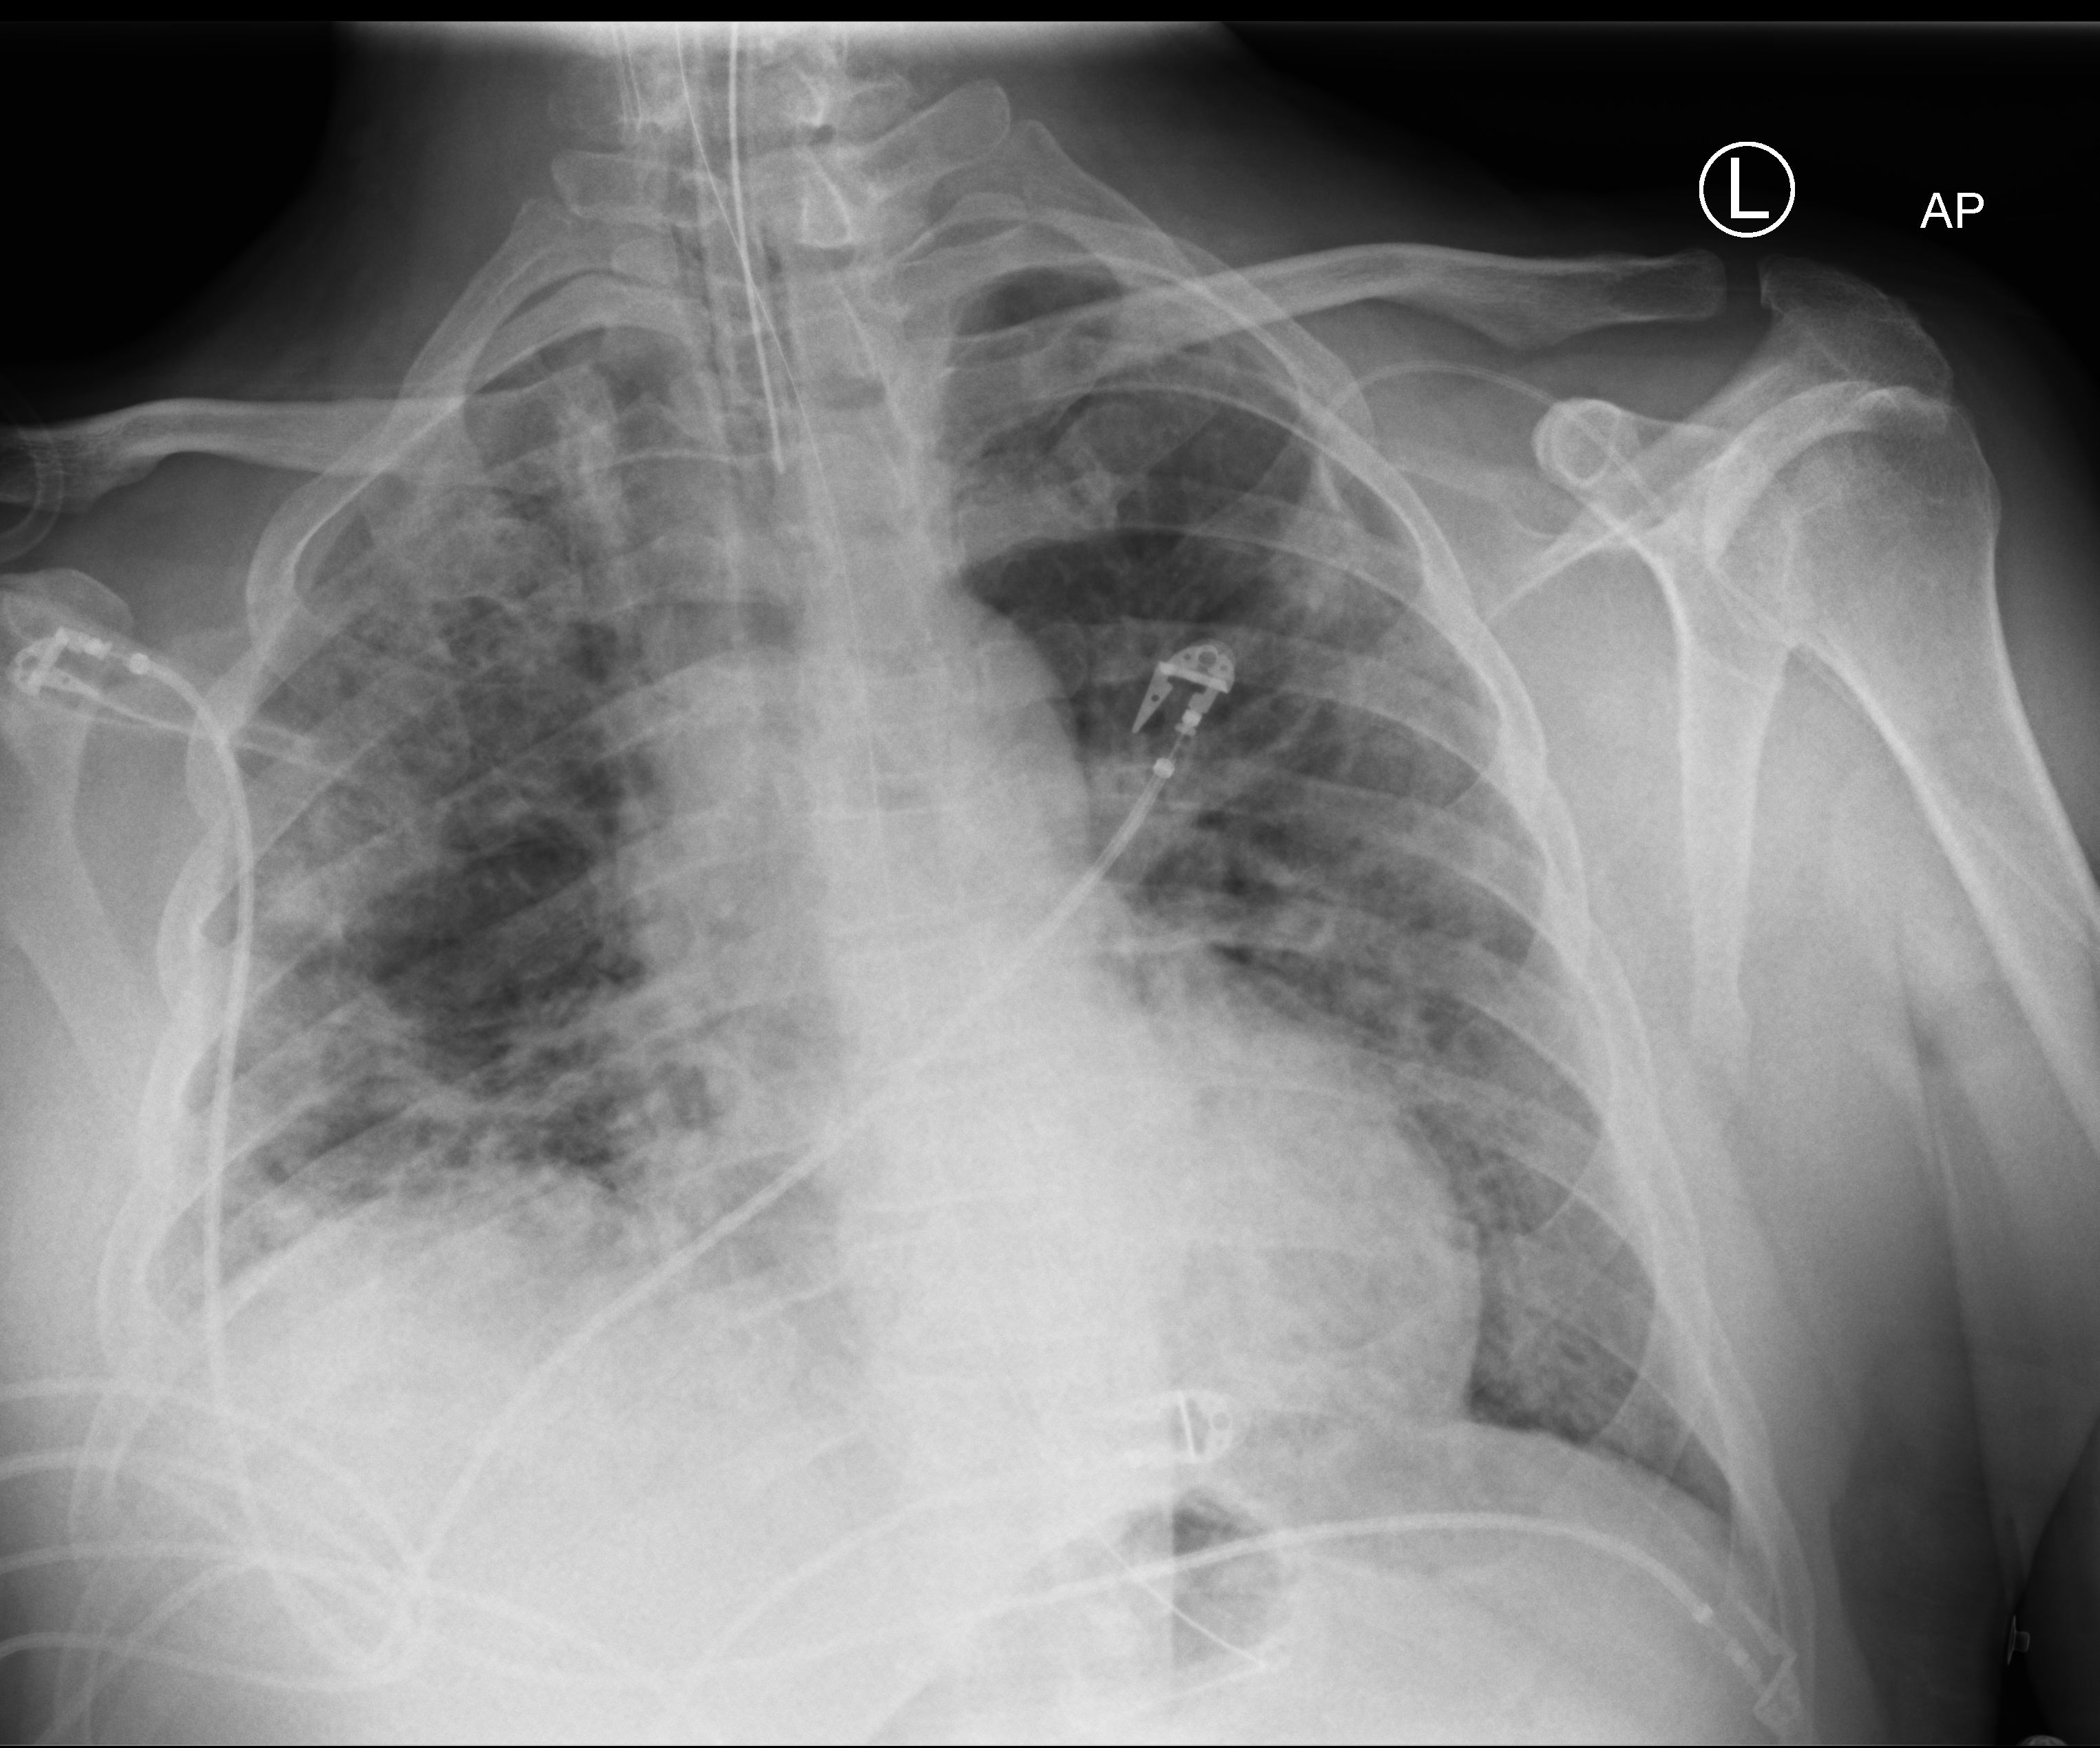
Bedside chest radiograph (computed radiography), anteroposterior (AP) projection. Patient hospitalised with COVID-19; male, aged 18–59 years.
From the hospital-stay record, not from the radiograph (when in the stay this image was taken is not recorded):
- length of hospital stay: 32 days
- mechanically ventilated during this hospital stay: yes
- admitted to intensive care during this hospital stay: no